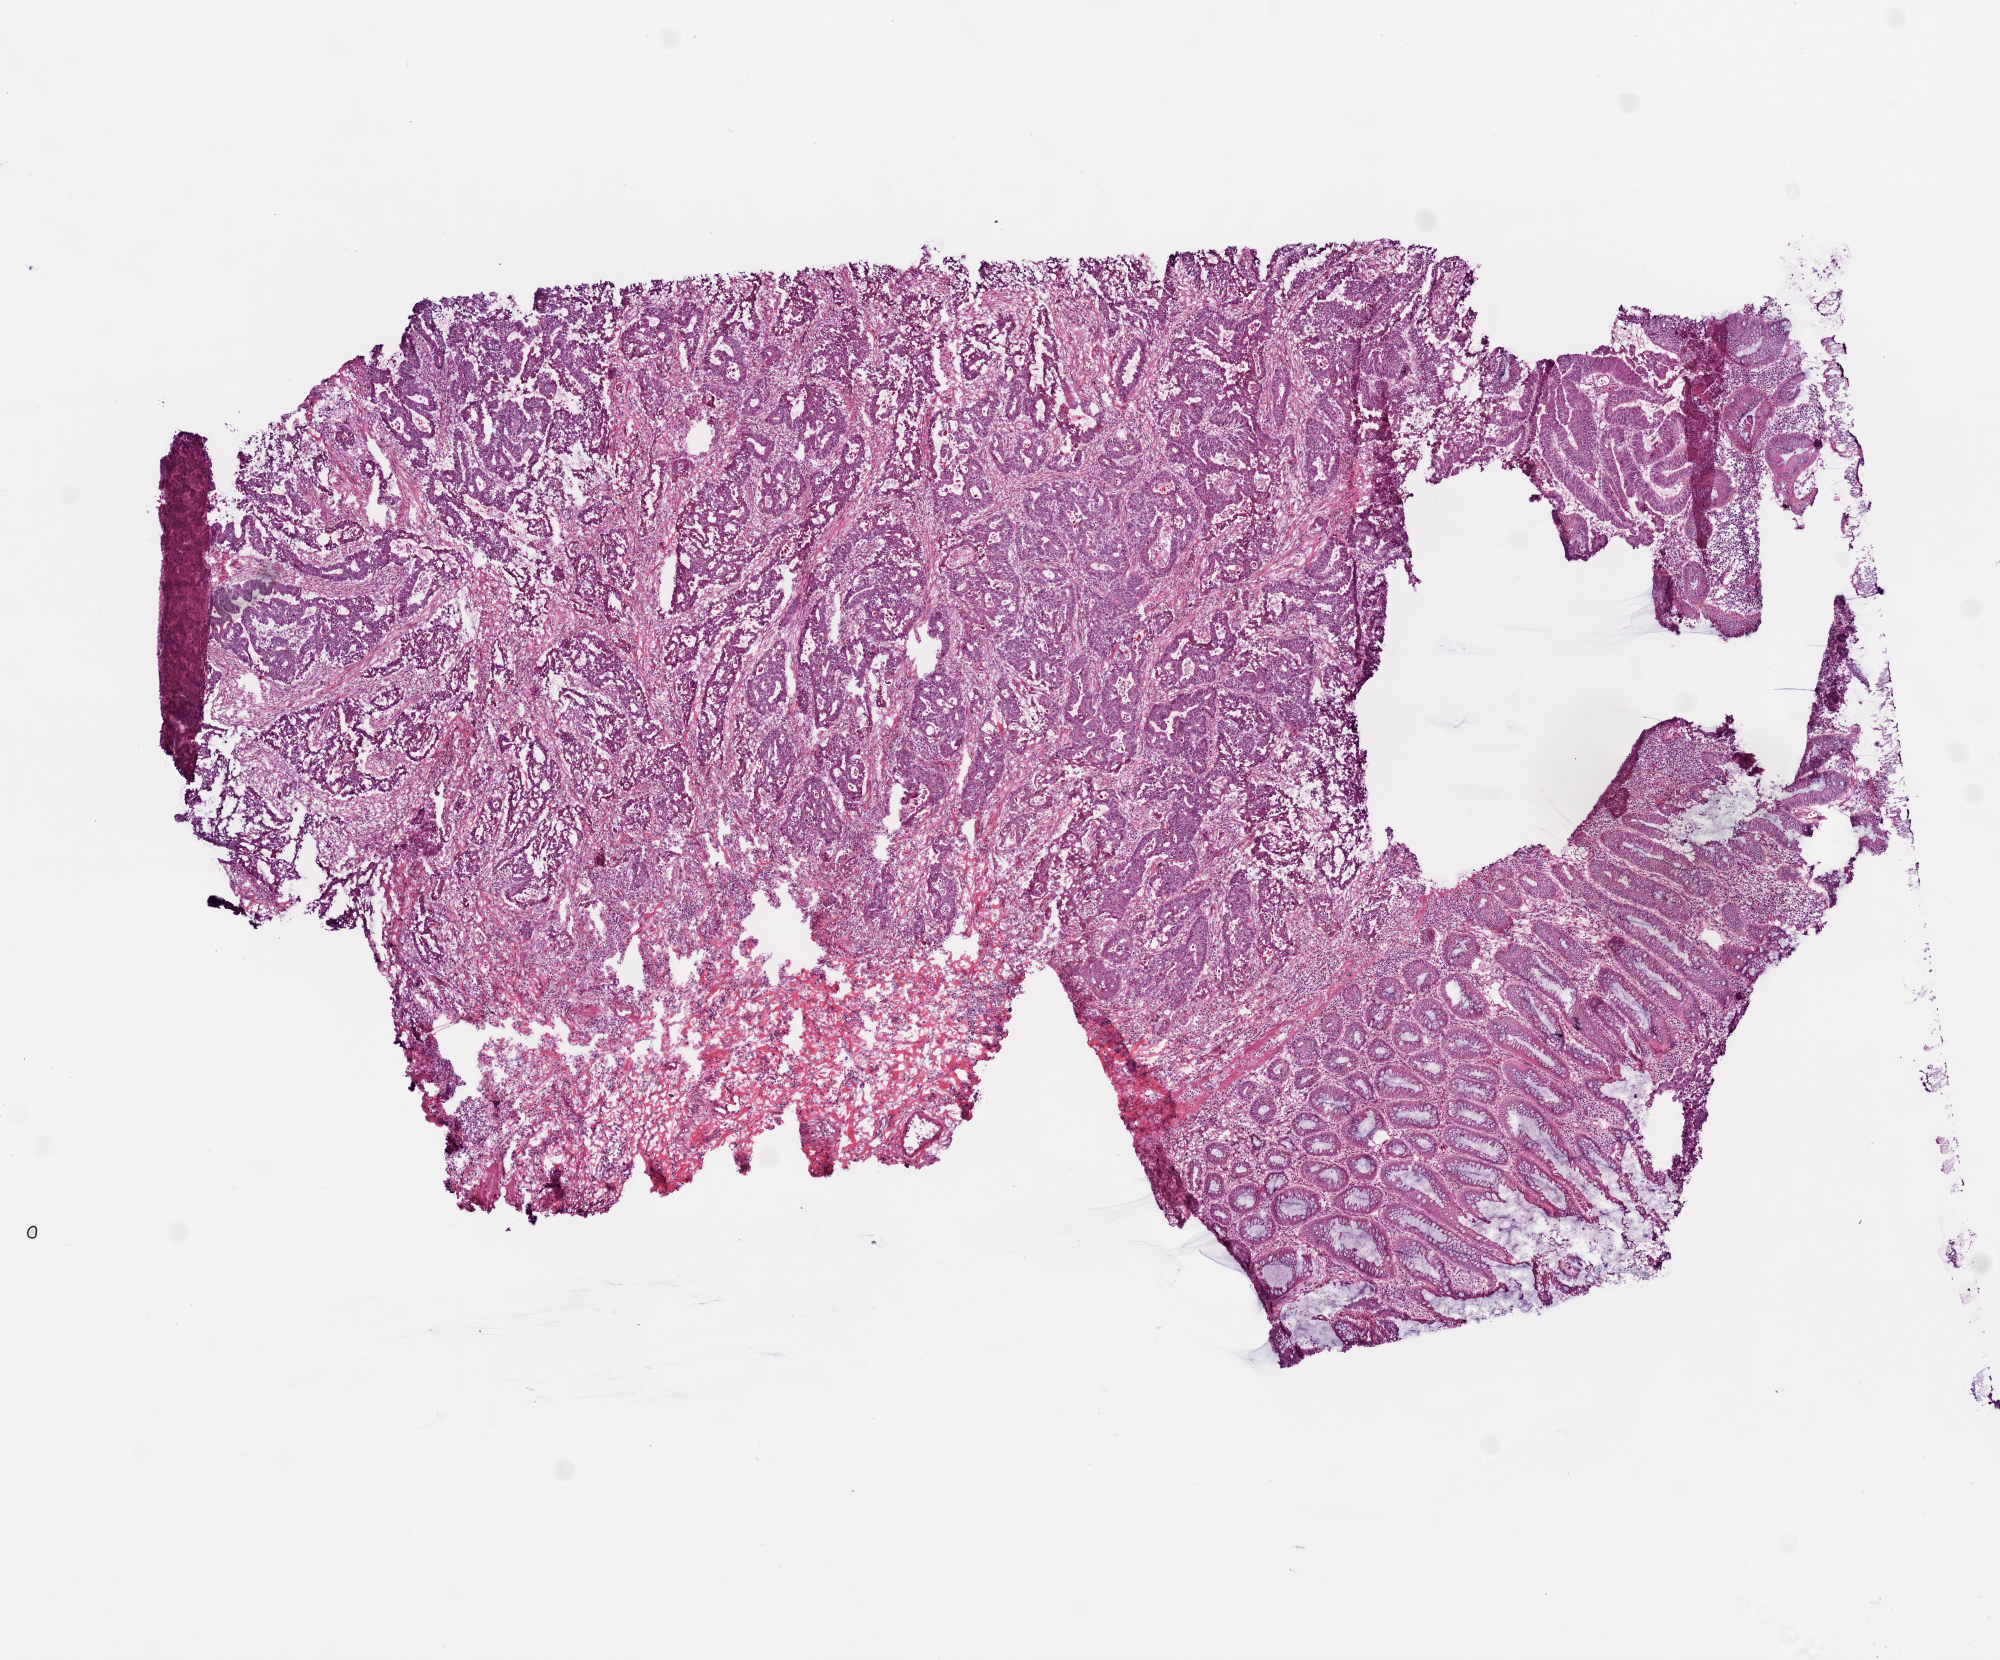
Whole-slide histology image, H&E — low-resolution overview of the scanned area, about 8.0 x 6.7 mm (slide scanned at 20x), frozen section, primary tumour sample from the colon. Female patient; age at initial diagnosis 74 years. Slide review estimates, as recorded: tumour cells 80%, tumour nuclei 80%, normal cells 0%, stromal cells 10%, necrosis 10%.
- AJCC pathologic stage: IIA
- lymph nodes positive (case pathology): 0 of 16 examined
- histologic diagnosis: Adenocarcinoma, NOS (sigmoid colon)